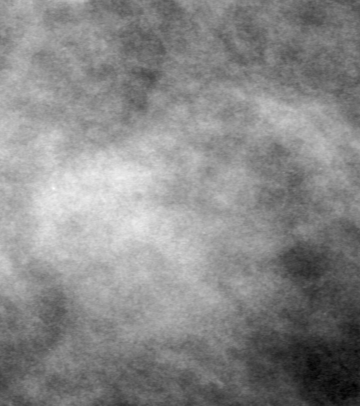
Cropped region of a digitized screen-film mammogram centred on a radiologist-marked abnormality, left breast, MLO view, BI-RADS breast density category 2 (scale 1–4).
- Marked abnormality: mass, shape oval, margins obscured; BI-RADS assessment category 4; subtlety rating 4 on a 1 (subtle) to 5 (obvious) scale; pathology (as recorded): malignant.